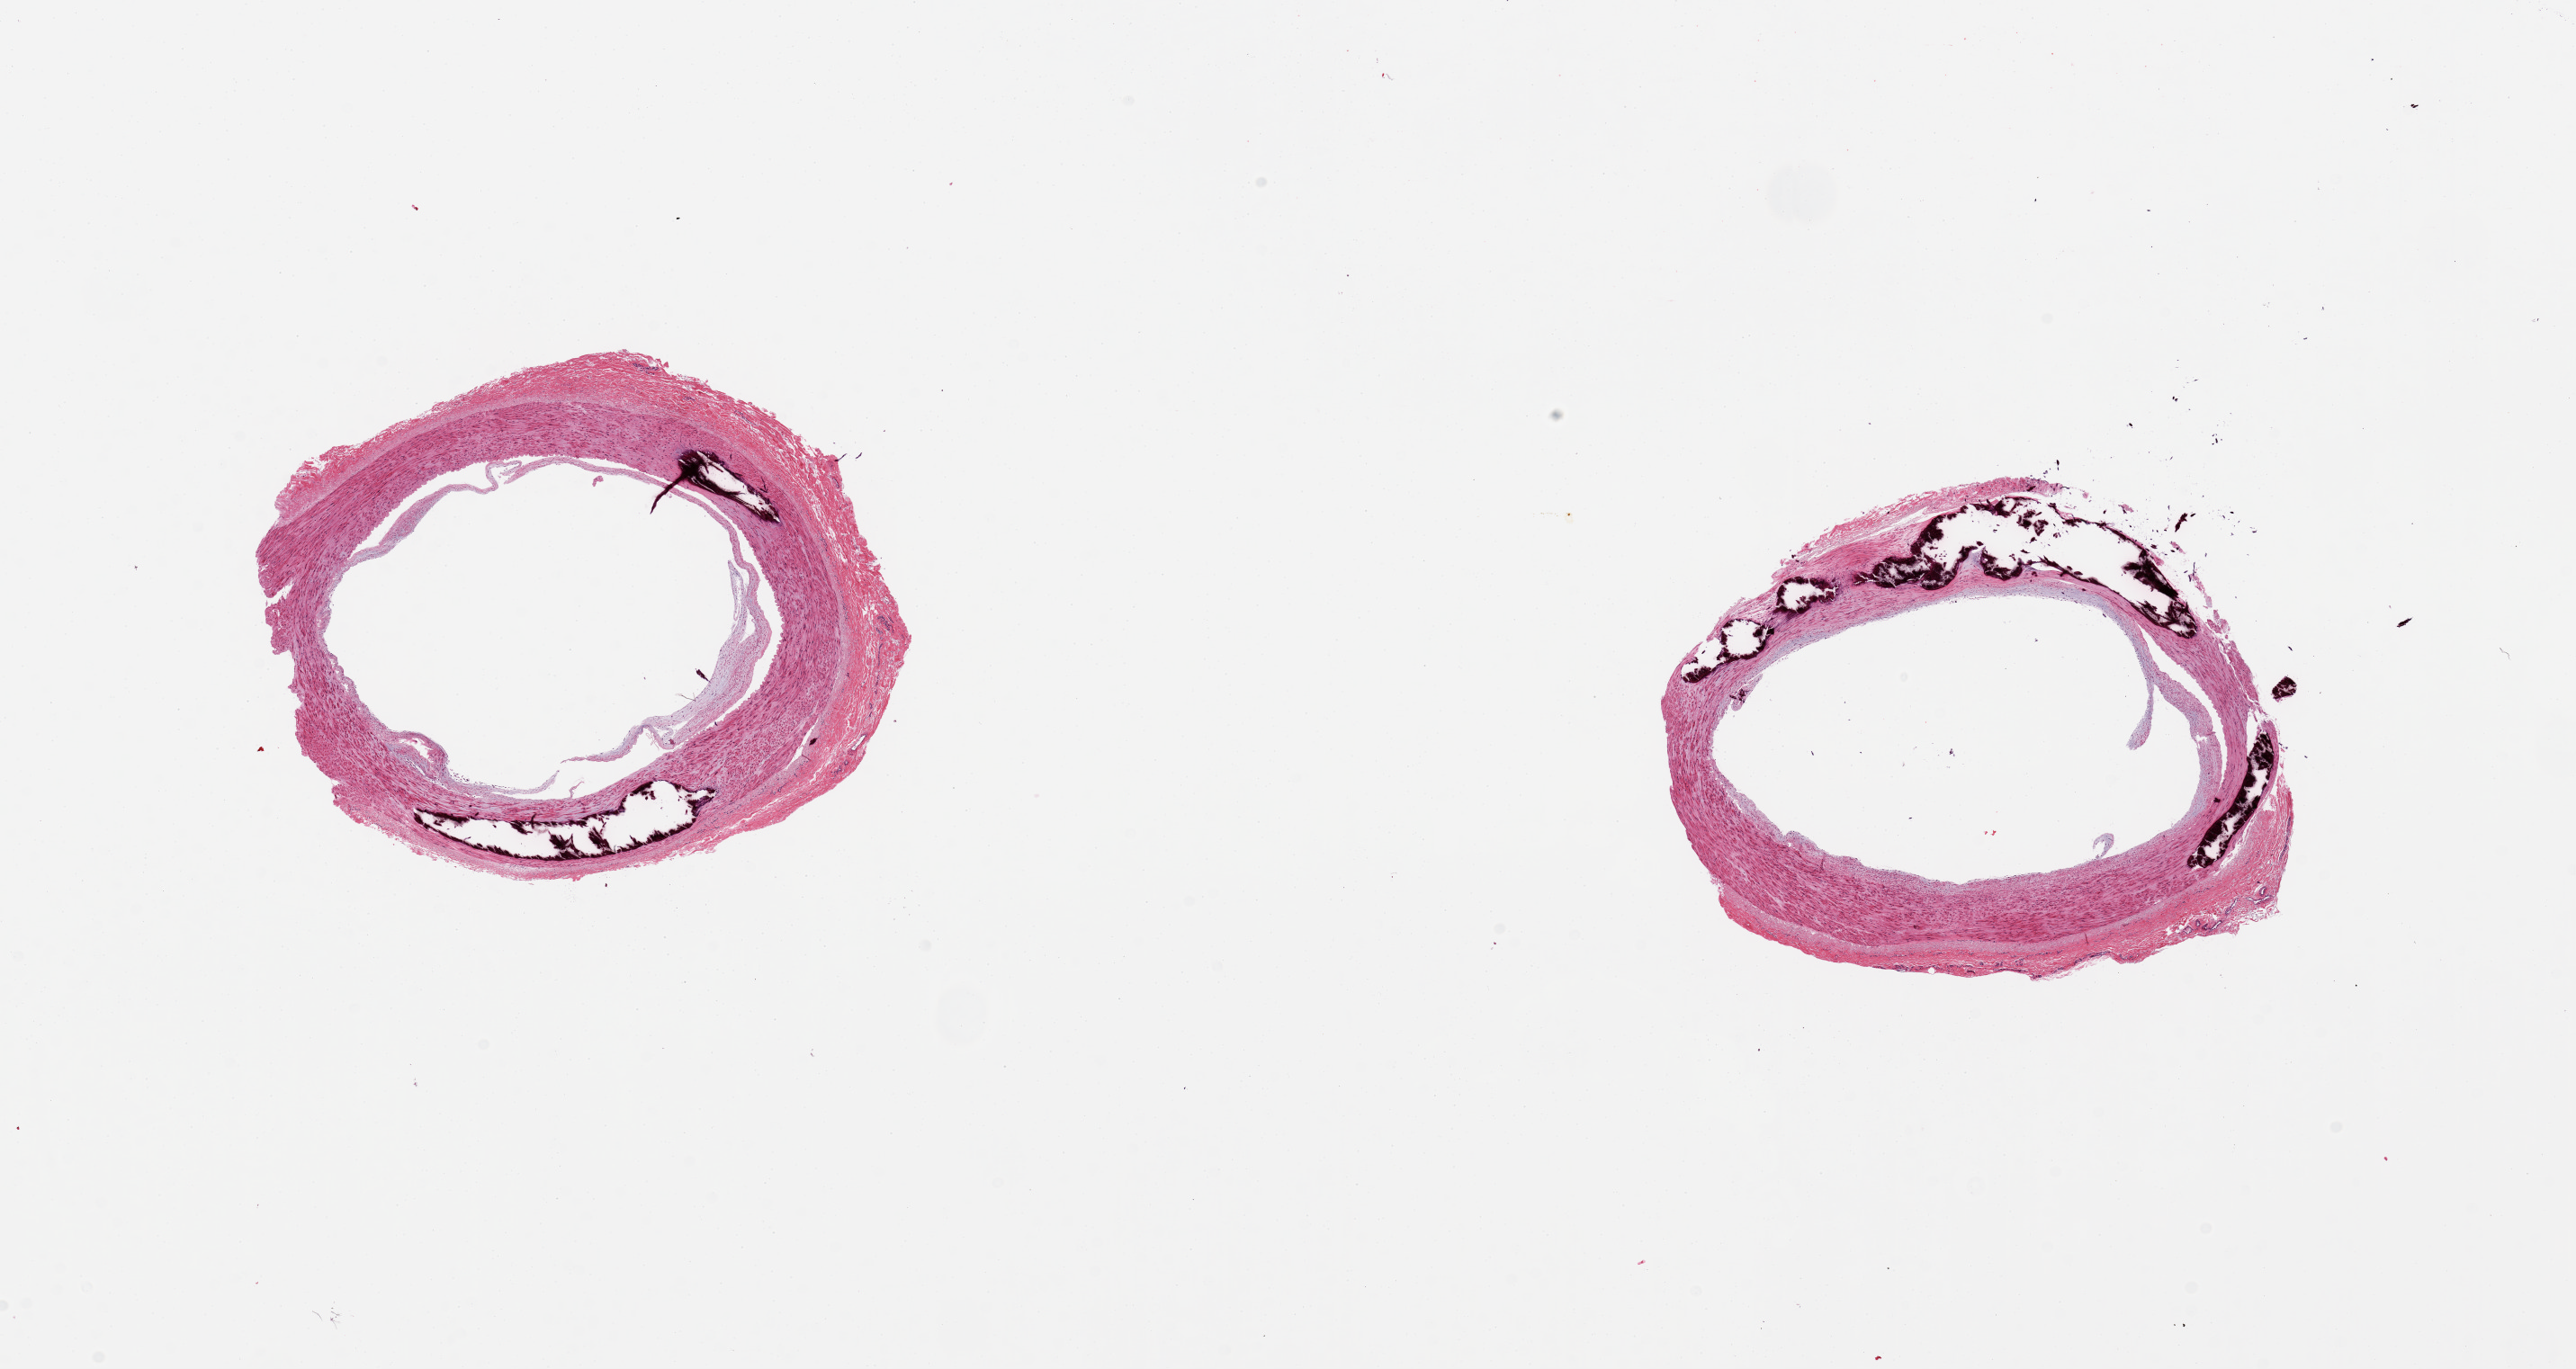
Whole-slide image, hematoxylin and eosin (H&E) stain, low-resolution overview of the scanned area, about 22.6 x 12.0 mm (from a 20x scan). PAXgene-fixed paraffin-embedded (PFPE) section. Target tissue: tibial artery. Donor tissue sample. Donor sex: male.
- reviewer comment on this tissue sample: 2 pieces; extensive medial calcification; no intimal plaques